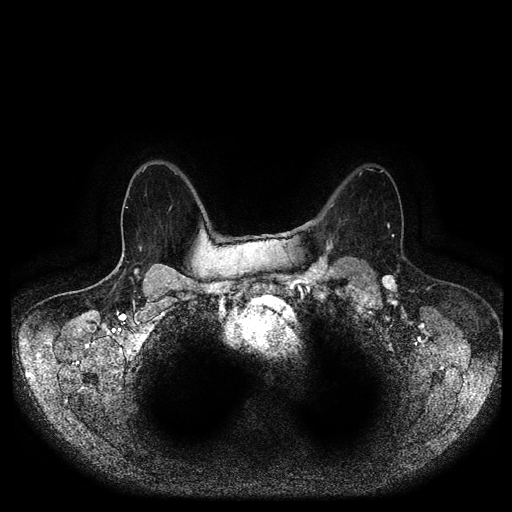
Breast MRI (dynamic contrast-enhanced, multi-phase), one axial slice; position 69 of 116 along the scan axis; dynamic contrast-enhanced series, time point 2 of 5 at this slice position (early post-contrast); 1.5 T; TE 2.6 ms, TR 5.2 ms; 2 mm slice thickness; 512 × 512 image matrix, field of view 380 × 380 mm. Female patient, age 69 years.
Annotated regions visible in this slice (semi-automatically segmented with operator editing):
- breast lesion (labelled 'tumour' in the annotation; benign lesions carry a separate 'benign' label): bounding box (x1, y1, x2, y2) in pixels: (304, 238, 333, 281)